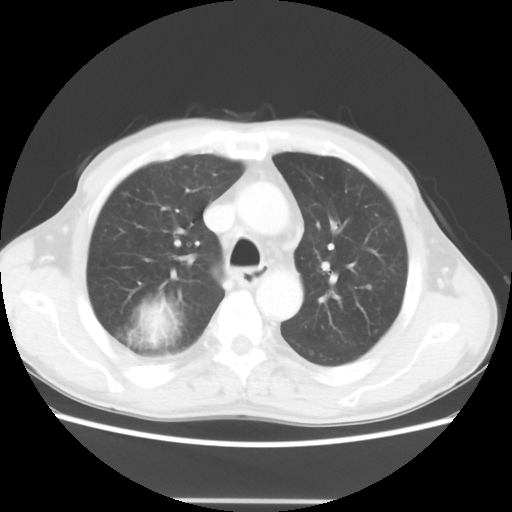
Chest CT, one axial slice; position 36 of 48 along the scan axis; 100 kVp; lung window (W 1500 / L -600 HU); 5 mm slice thickness; 512 × 512 image matrix, field of view 361 × 361 mm. Male patient, age 66 years. From the clinical record (not read from this slice): clinical TNM (as recorded): T4 N1 M1; histopathological grade: G3.
Annotated regions visible in this slice (rectangle marked by the reading radiologist):
- lung tumour (recorded histology: small cell carcinoma): bounding box (x1, y1, x2, y2) in pixels: (133, 292, 181, 347)